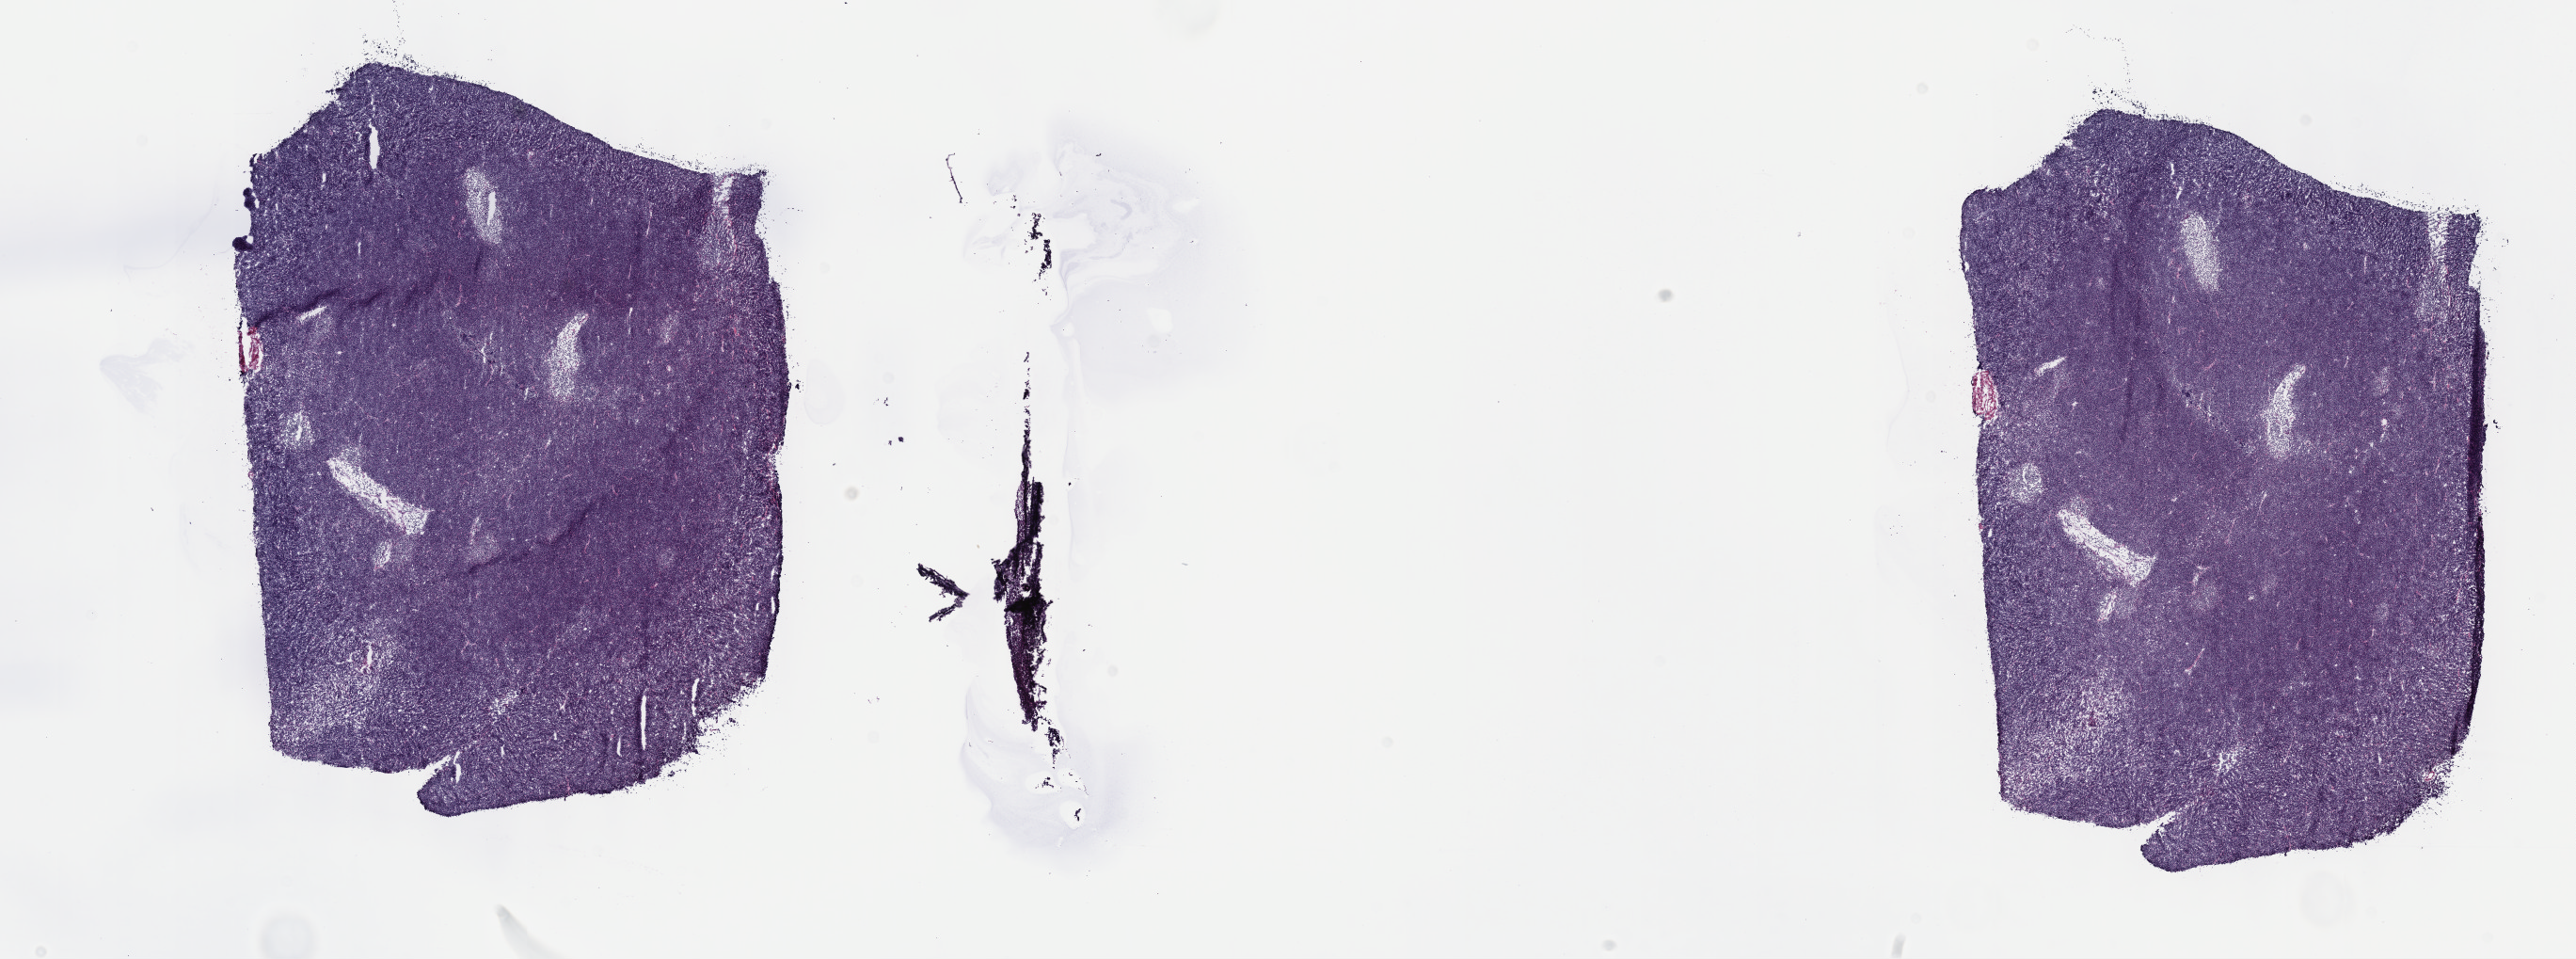
Digitized H&E-stained tissue section (whole slide), whole scanned area (about 22.1 x 8.2 mm) shown as a low-resolution overview; frozen section from the top of the tissue portion; primary tumour sample from the thymus. Male, age 73 years at initial diagnosis. Pathologist review of this section (percent, as recorded): tumour cells 100%, tumour nuclei 80%, normal cells 0%, stromal cells 0%, necrosis 0%. Inflammatory infiltration, as recorded: lymphocyte infiltration 2%, monocyte infiltration 0%, neutrophil infiltration 0%.
• diagnosis: Thymoma, type B1, malignant (anterior mediastinum)